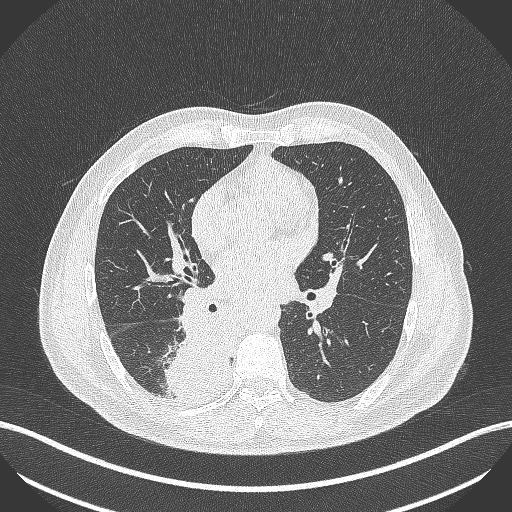
Chest CT, one axial slice; slice 237 of 451 in the series (ordered by position); lung window (W 1500 / L -600 HU); 1 mm slice thickness; 512 × 512 image matrix, field of view 400 × 400 mm. Male patient, age 61 years. Case-level facts recorded for this patient, not image findings: clinical TNM (as recorded): T1 N0 M0; histopathological grade: G3.
Outlined on this slice (rectangle marked by the reading radiologist):
- lung tumour (recorded histology: small cell carcinoma): bounding box (x1, y1, x2, y2) in pixels: (162, 311, 234, 404)